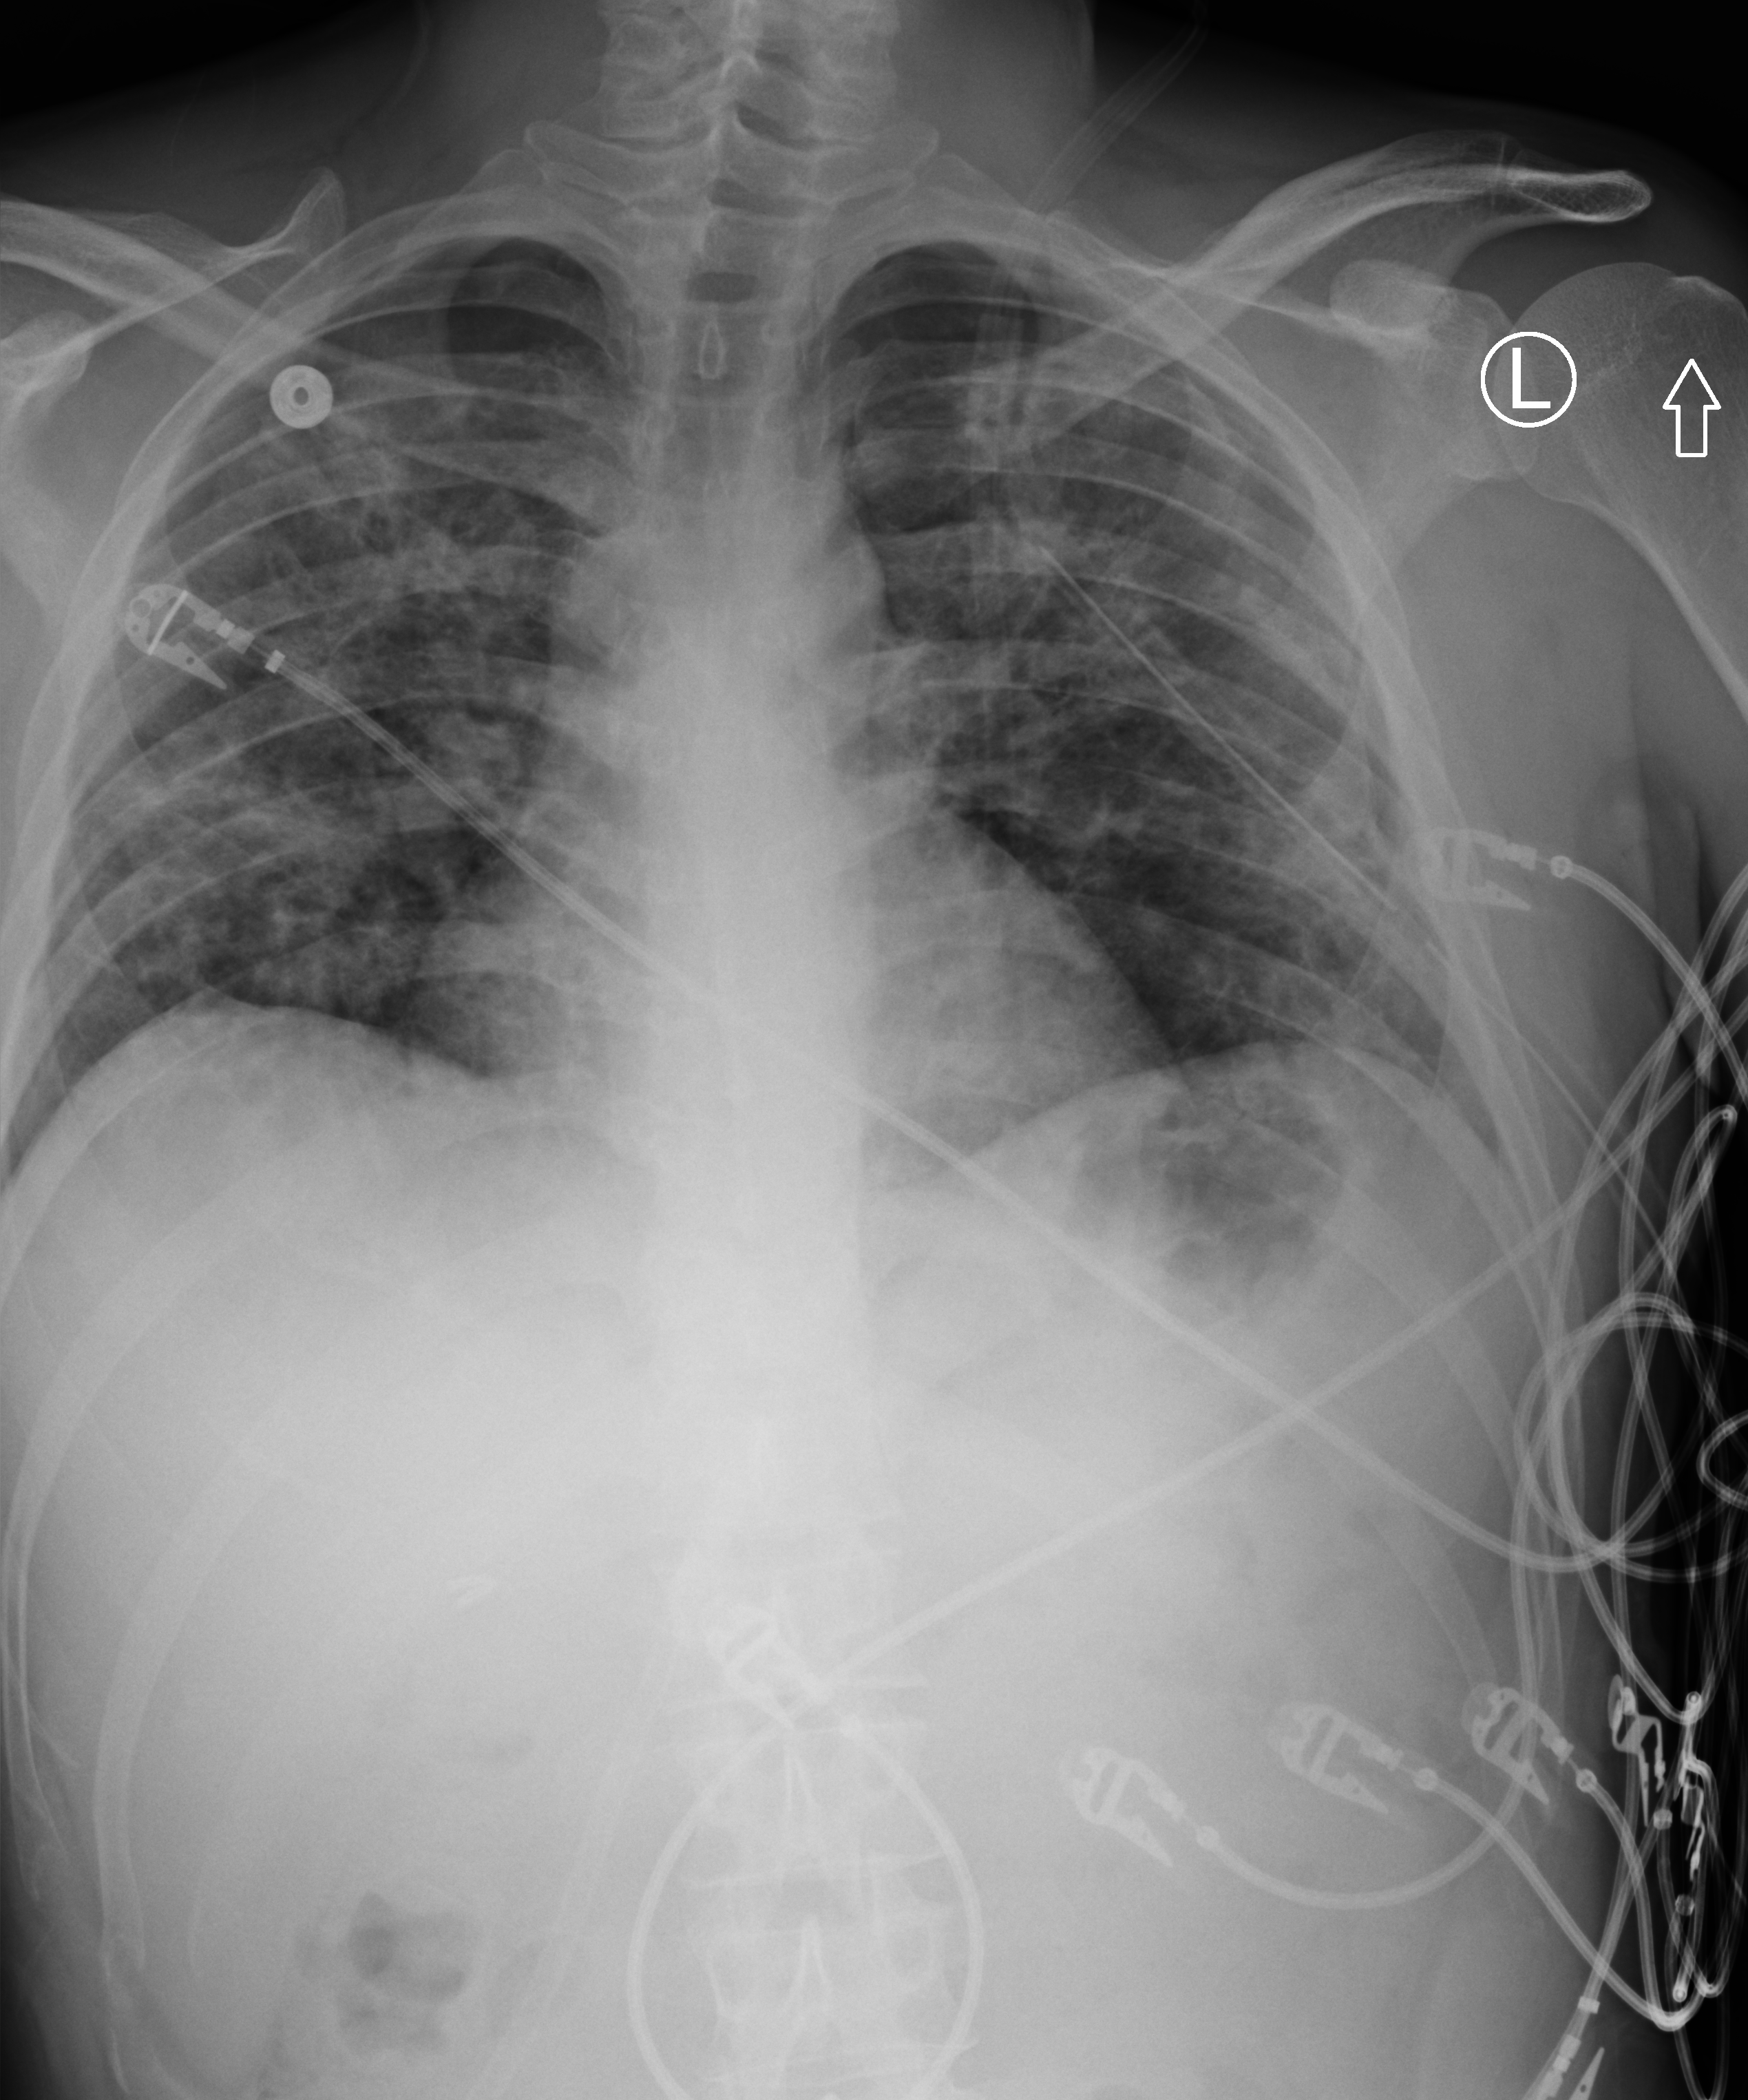
Chest X-ray (portable). Patient hospitalised with COVID-19; male, aged 18–59 years.
Hospital-stay facts (about this admission, not read from this image; timing relative to this image not recorded):
- mechanically ventilated during this hospital stay: yes
- length of hospital stay: 29 days
- diabetes (admission record): no